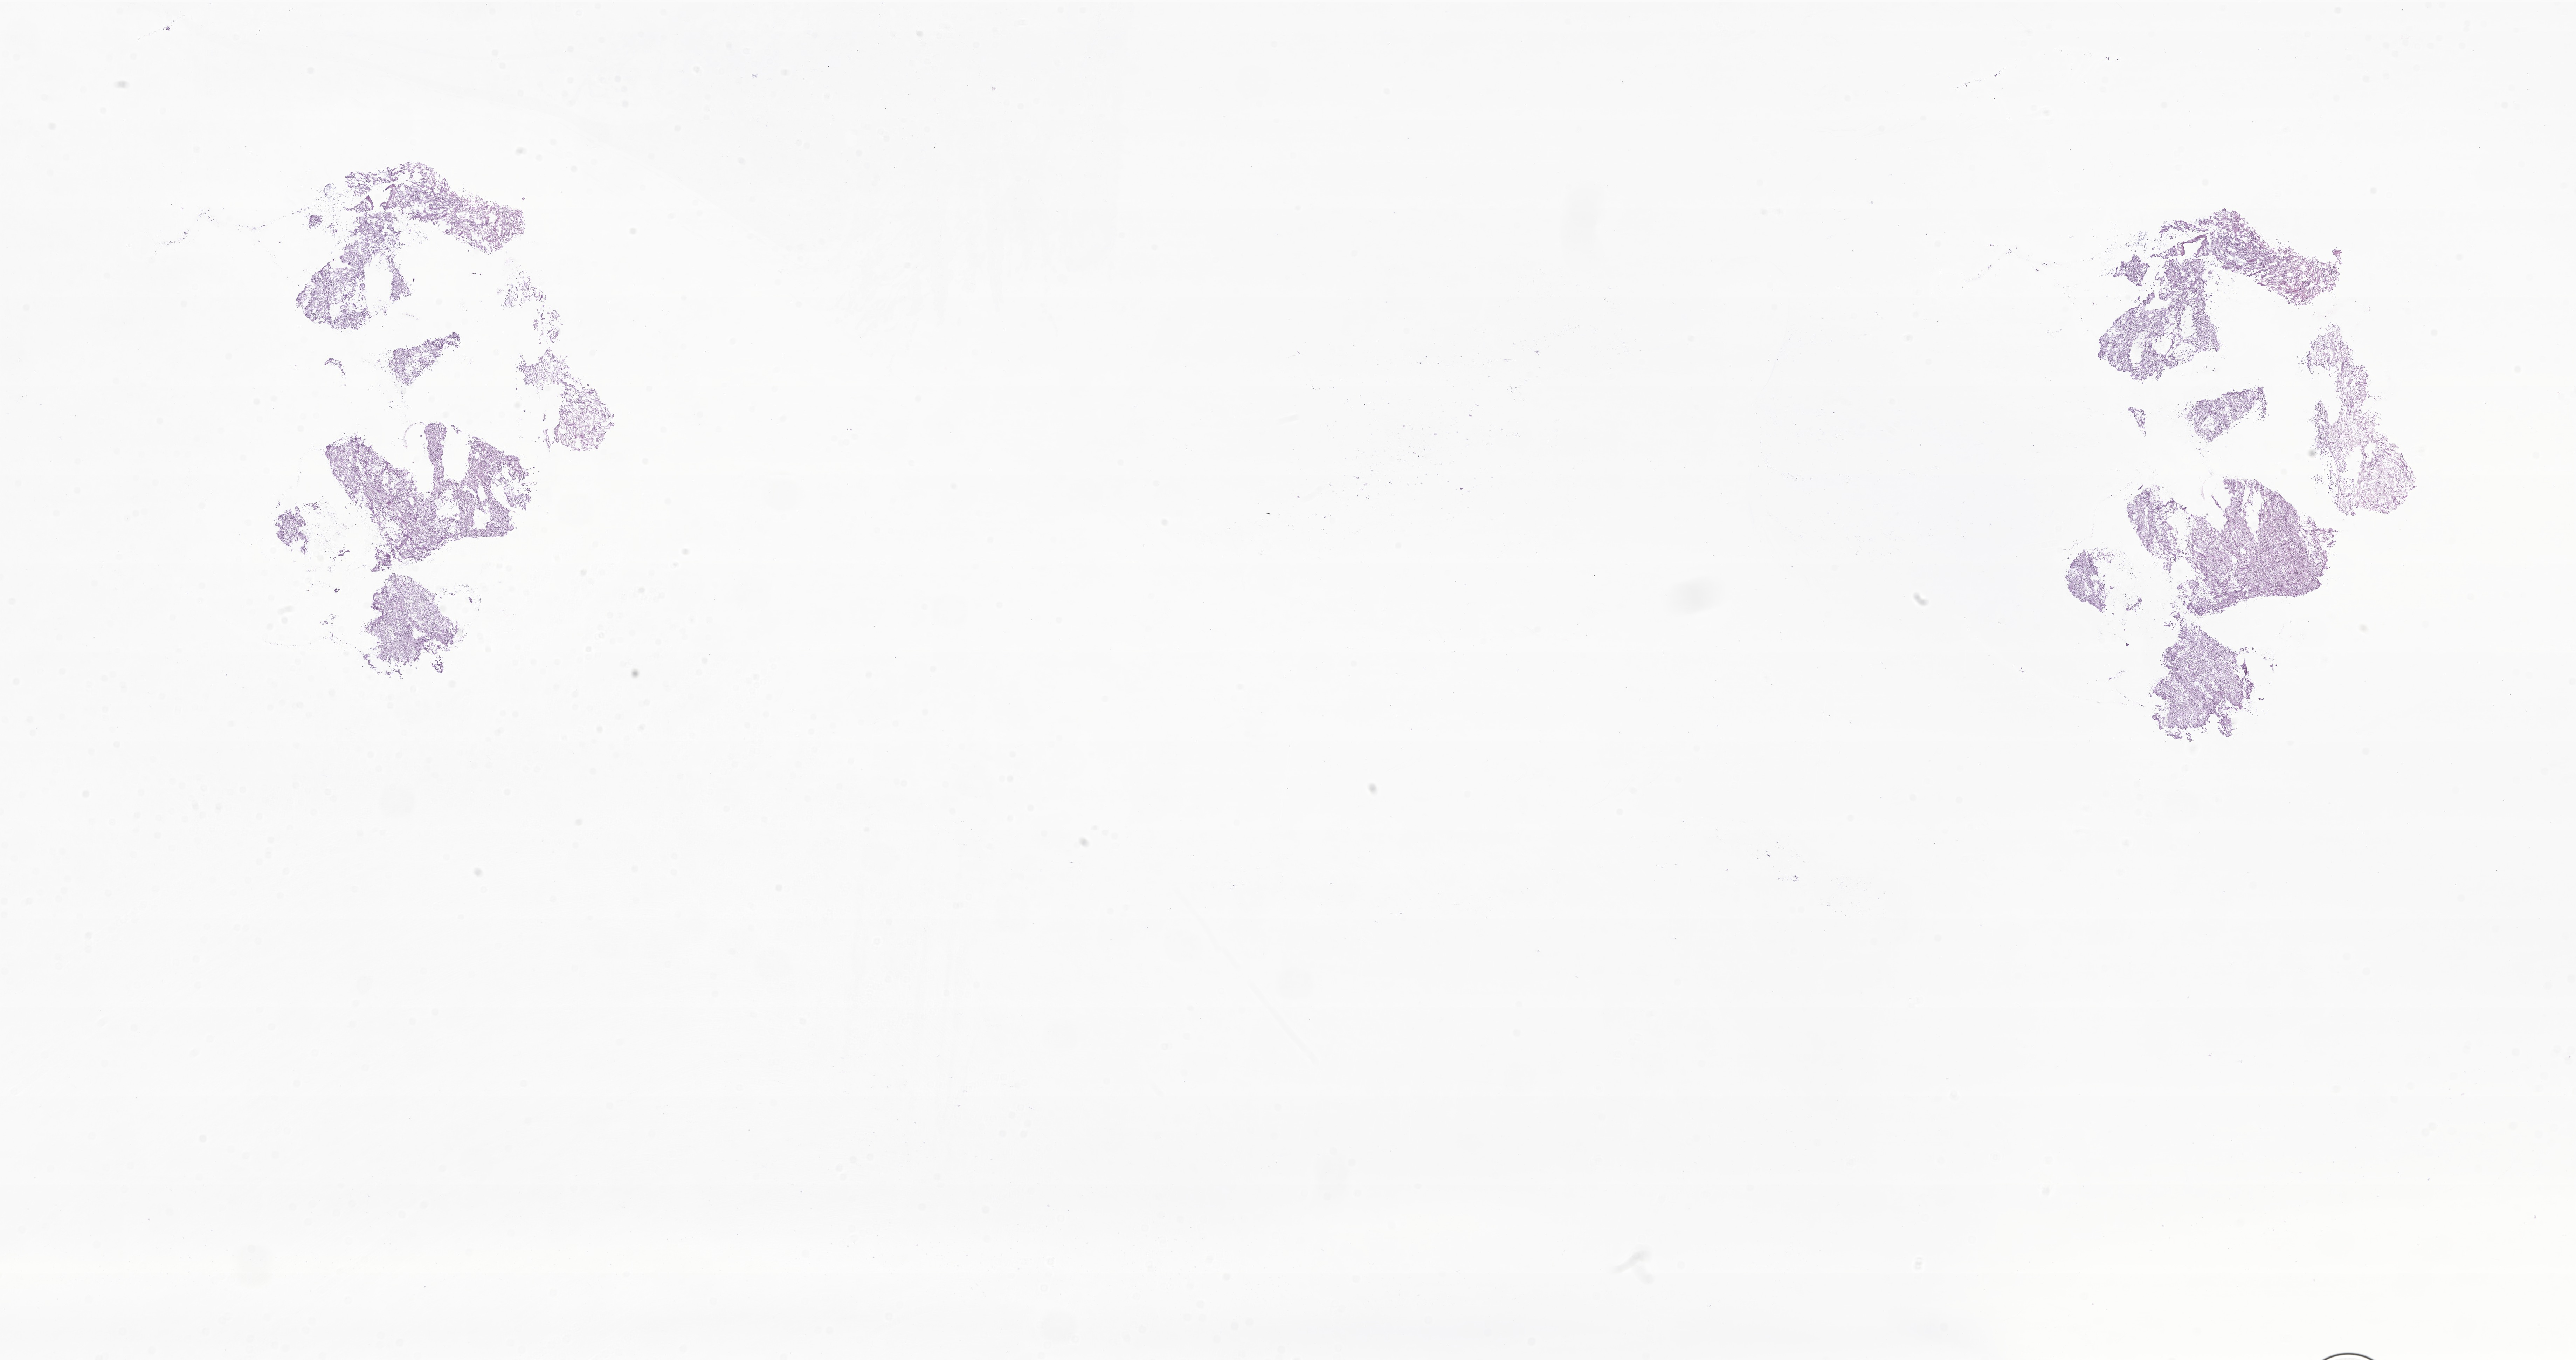
Hematoxylin and eosin (H&E) whole-slide image of tumor tissue from the brain — a low-resolution overview of the entire scanned area, about 31.0 x 16.4 mm; frozen section (OCT-embedded). Patient: female, age 203 months (16 years 11 months).
• diagnosis: Pleomorphic xanthoastrocytoma, NOS